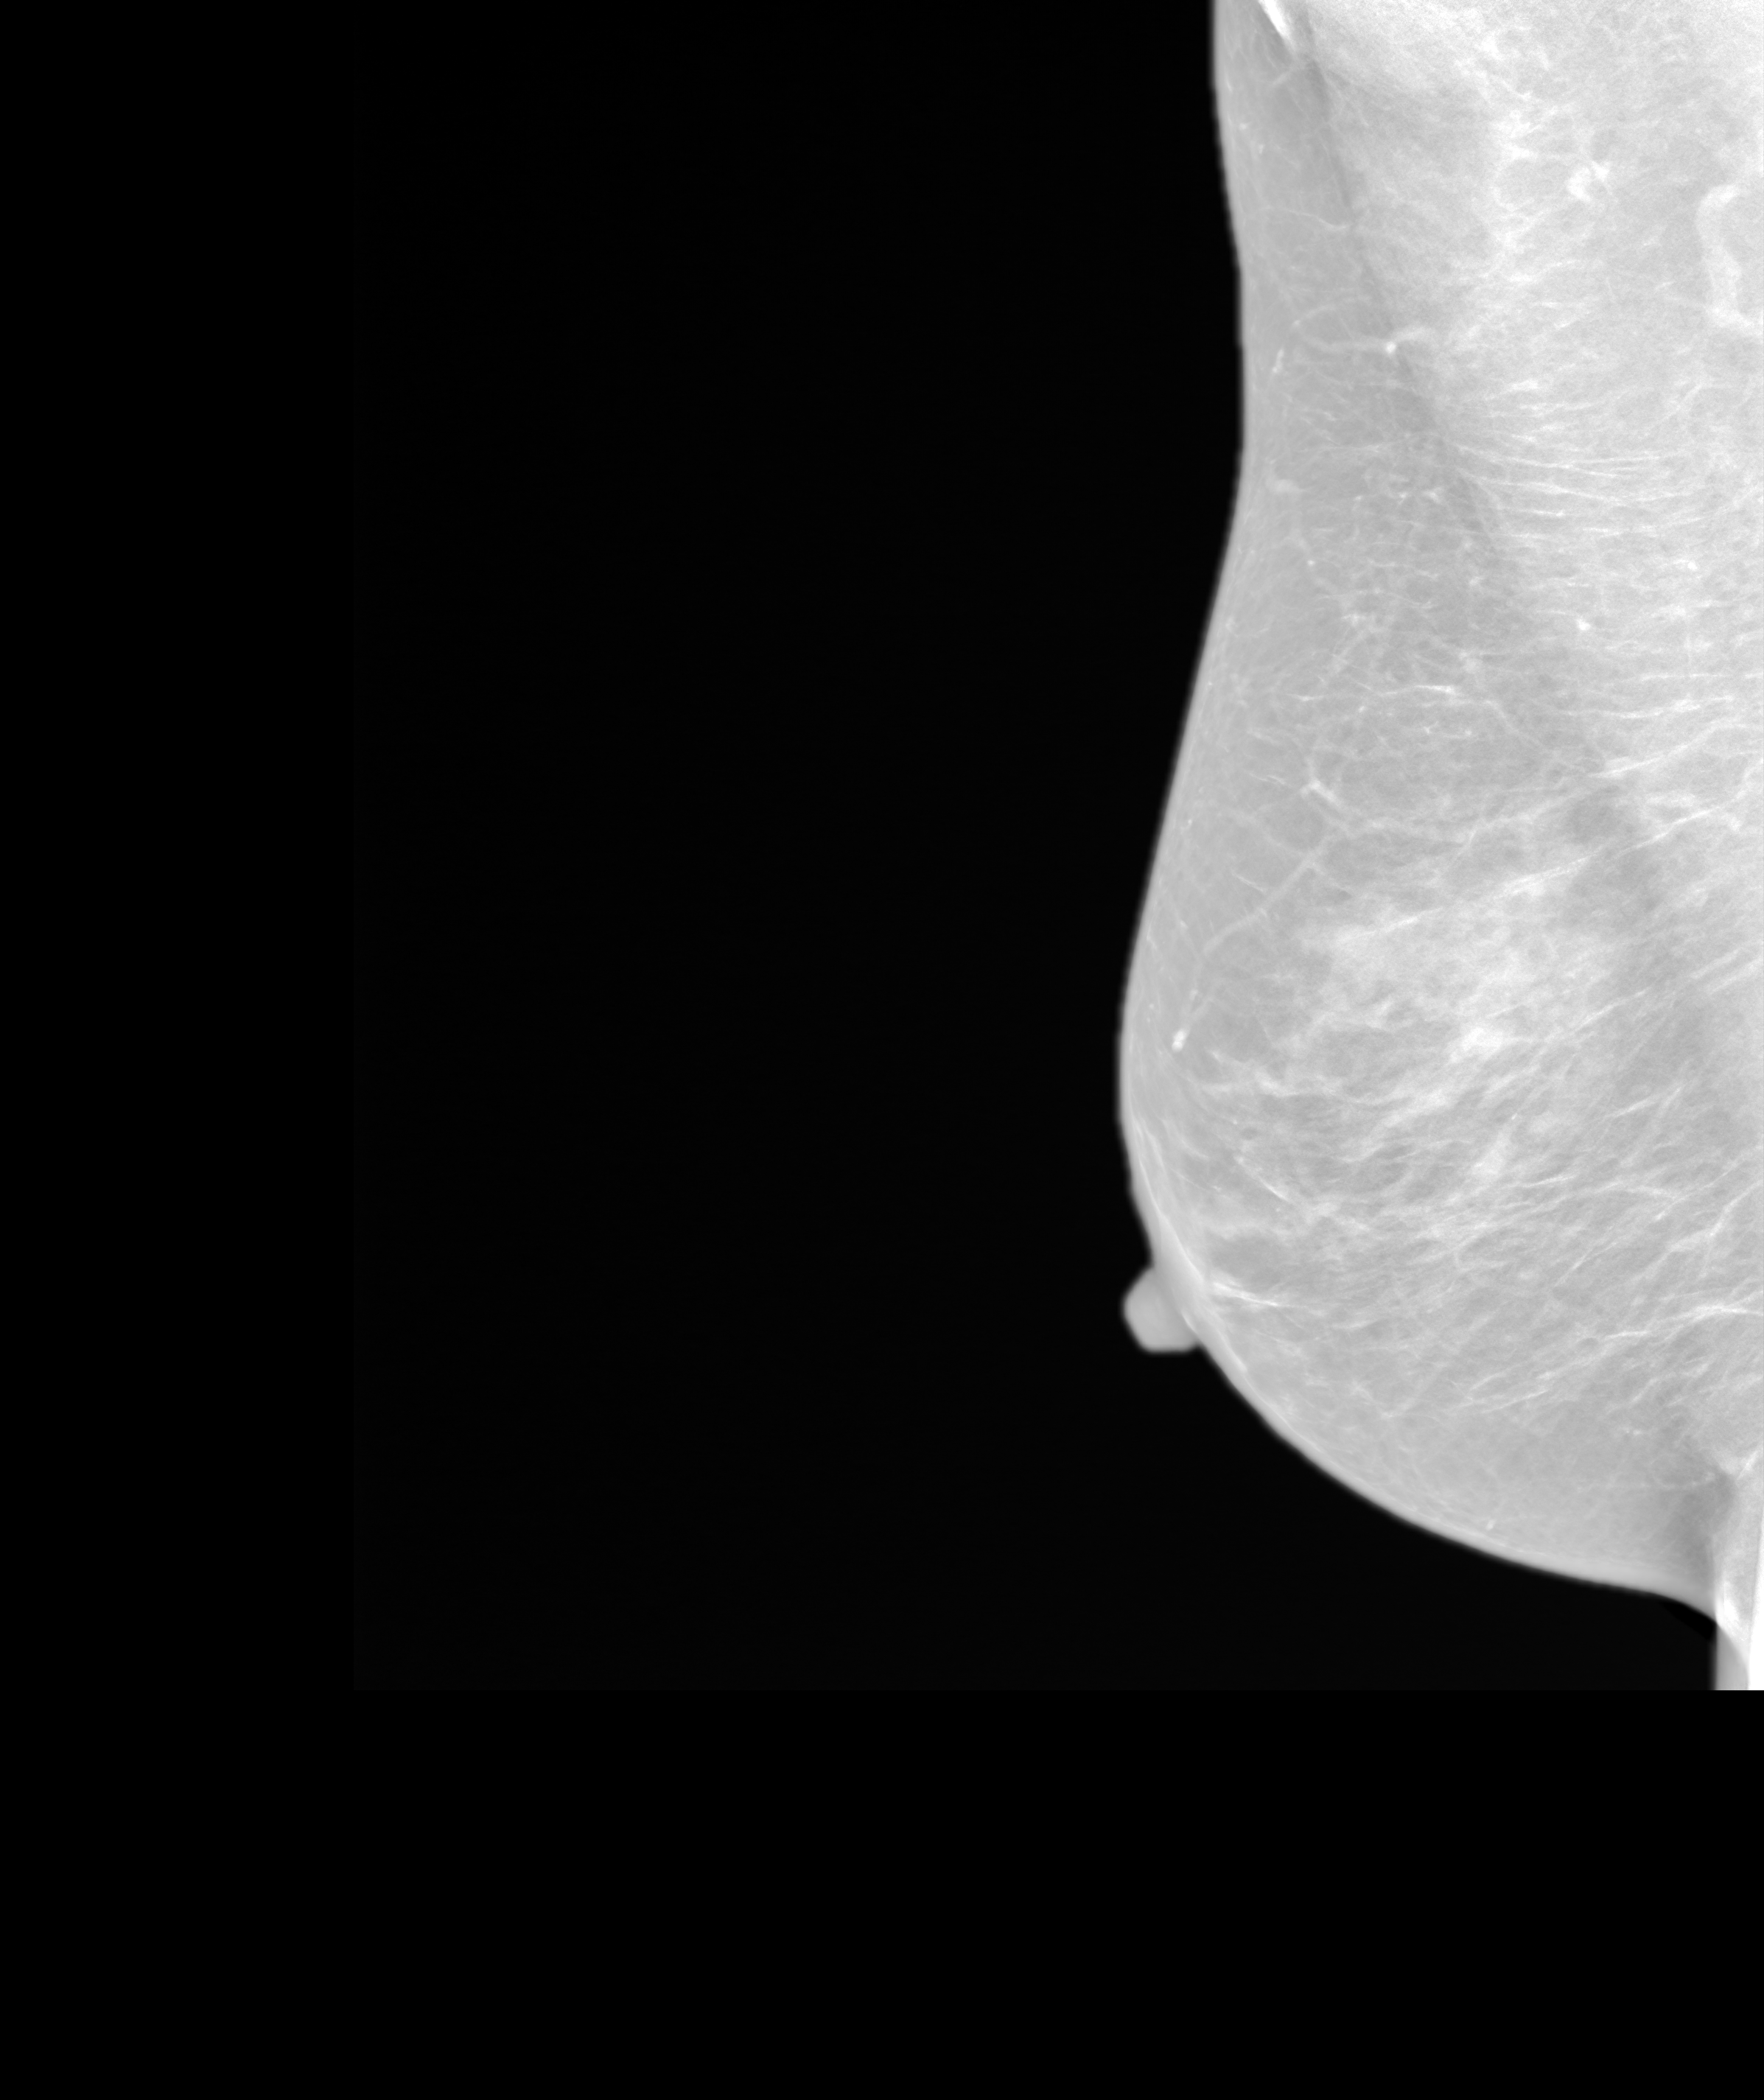
Annual screening mammography examination; system: SenoIris_1SP1.1(421). Patient: female, 49 years.
Image type: synthesized 2-D view from tomosynthesis. Breast: right. Projection: medio-lateral oblique projection.